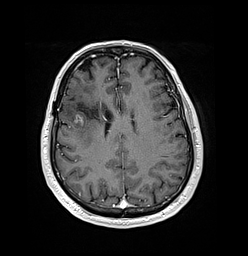
Brain MRI from a brain-tumour surgery series, one axial slice; position 60 of 176 along the scan axis; T1-weighted post-contrast; 1 mm slice thickness; 248 × 256 image matrix, field of view 242 × 250 mm. From the clinical record (not read from this slice): histopathology: Oligodendroglioma; WHO grade: 3; IDH mutation: yes.
Annotated regions visible in this slice (expert manual segmentation):
- tumour: bounding box <73,113,85,126> (left, top, right, bottom; pixels)